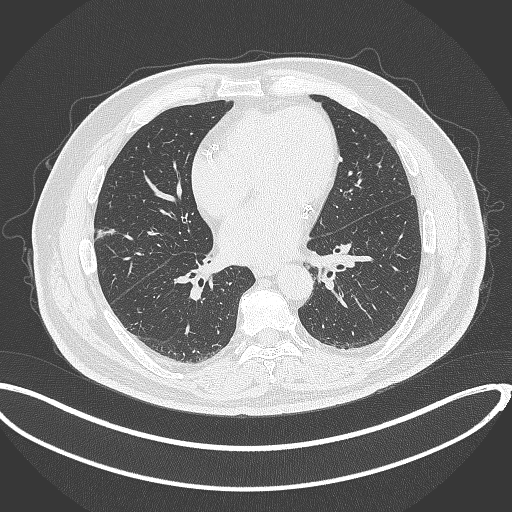
Chest CT, one axial slice; position 143 of 340 along the scan axis; reconstruction kernel B70f; lung window (W 1500 / L -600 HU); 1 mm slice thickness; 512 × 512 image matrix, field of view 427 × 427 mm. Male patient, age 68 years. From the clinical record (not read from this slice): clinical TNM (as recorded): T1c N0 M0; histopathological grade: G2.
Structures marked on this image (bounding box drawn by a radiologist):
- lung tumour (recorded histology: adenocarcinoma): bounding box <94,226,116,240> (left, top, right, bottom; pixels)